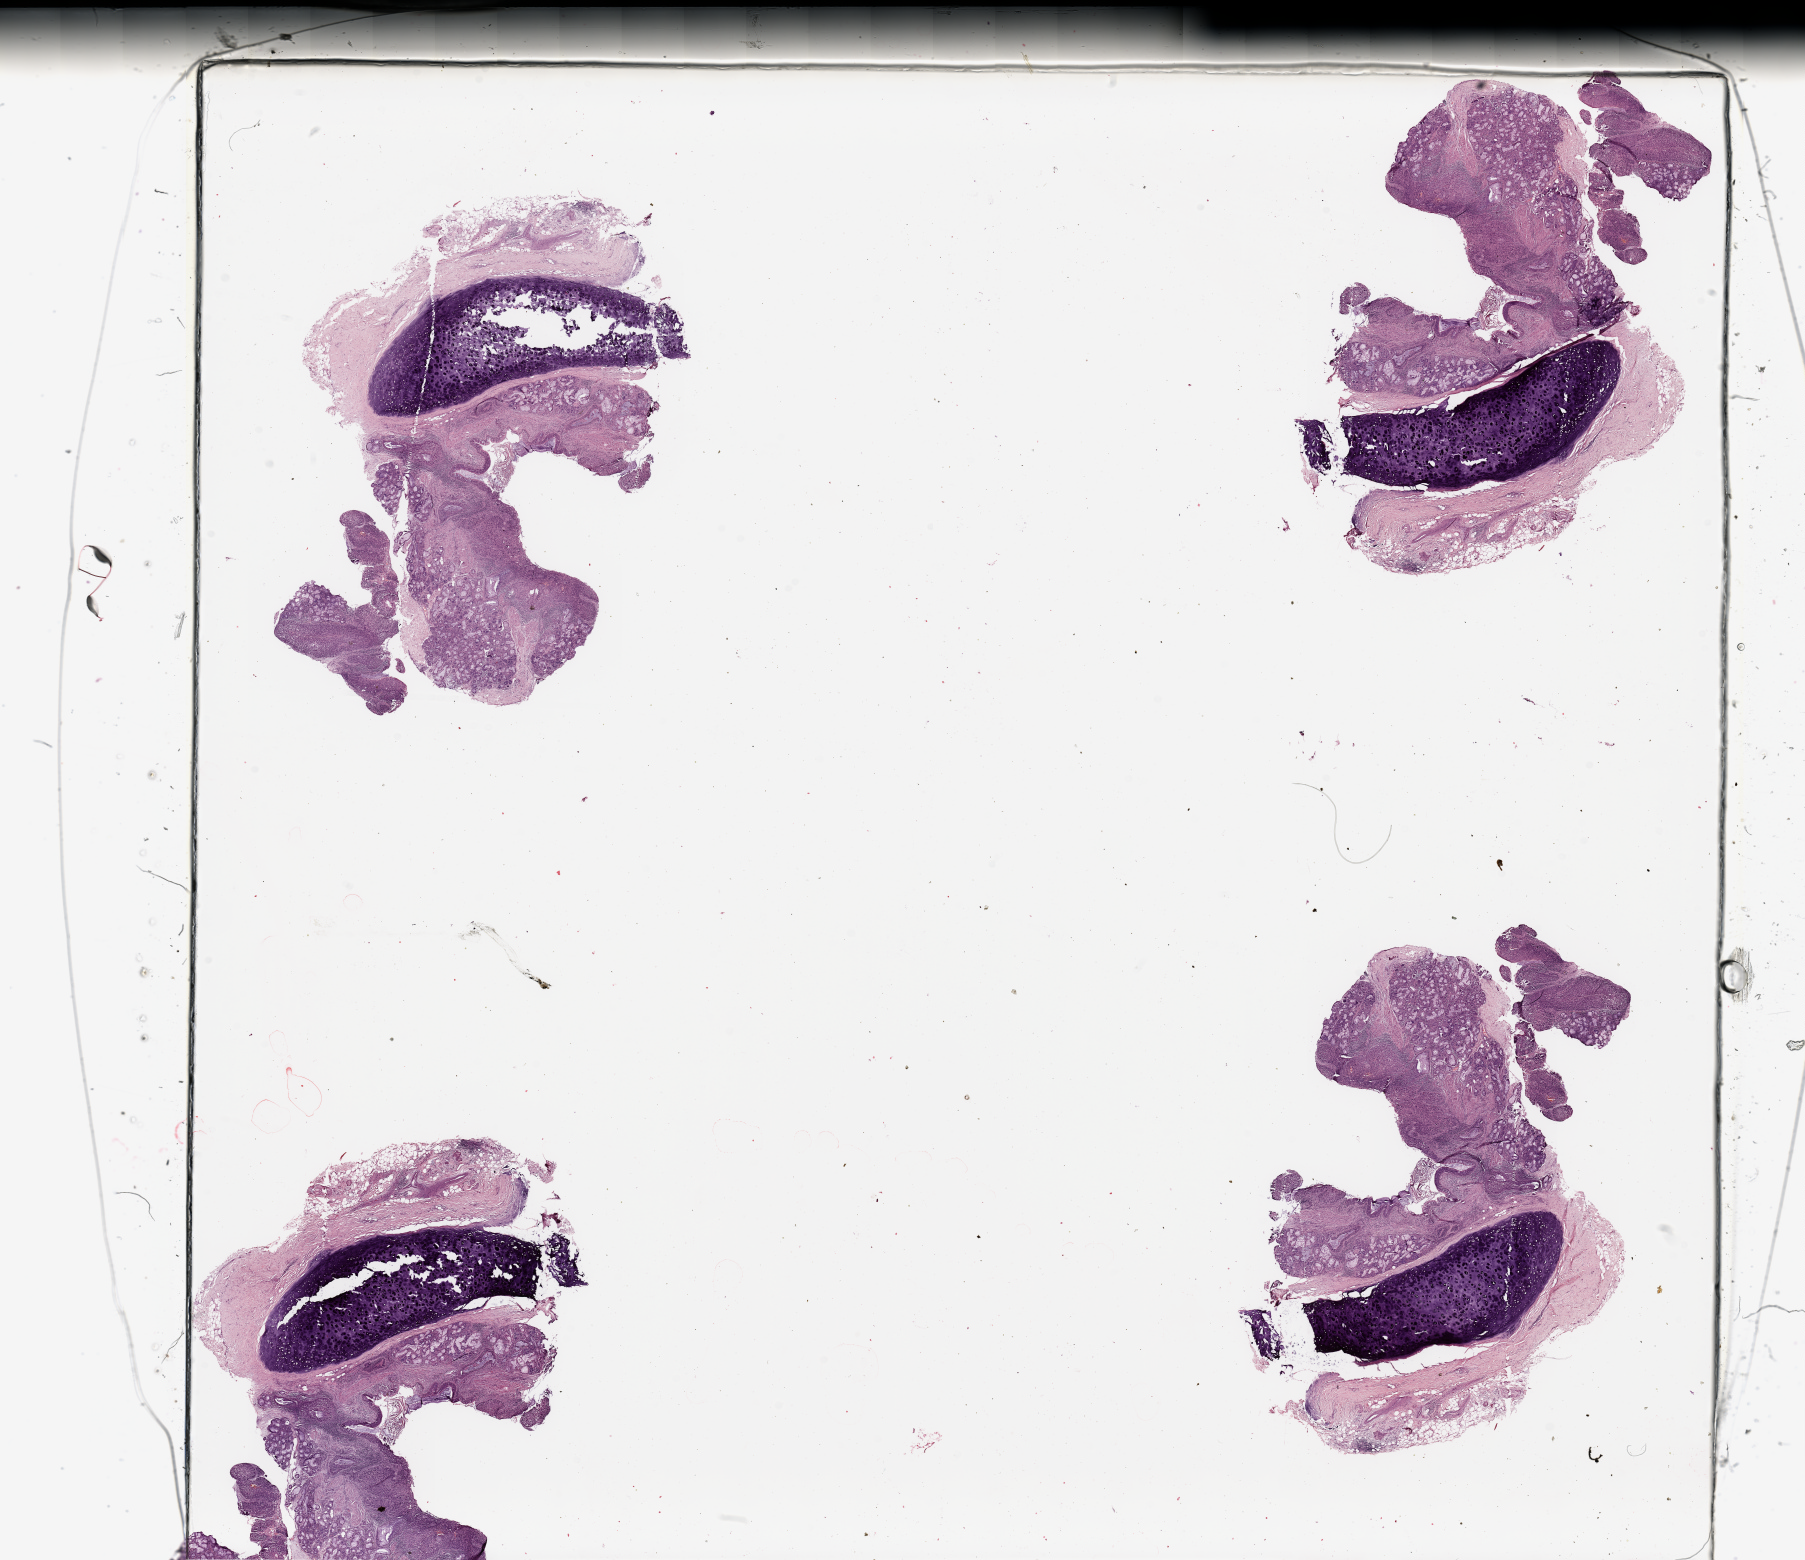
Digitized H&E-stained tissue section (whole slide) — low-resolution overview of the scanned area, about 28.5 x 24.7 mm. Tumour tissue sample, lung. 46-year-old male patient. Histologic grade: G2 (moderately differentiated).
• AJCC pathologic stage: IIA
• primary tumour site (as recorded): left upper lobe
• diagnosis: Squamous cell carcinoma, NOS